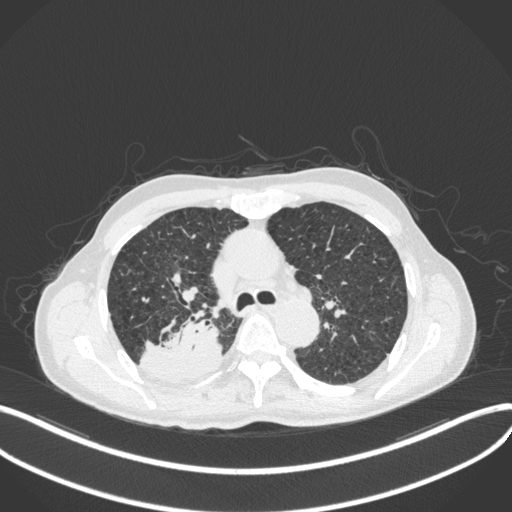
Chest CT, one axial slice; slice 305 of 423 in the series (ordered by position); lung window (W 1500 / L -600 HU); 512 × 512 image matrix. Patient: male, 79 years. Case-level facts recorded for this patient, not image findings: clinical TNM (as recorded): T3 N0 M0.
Outlined on this slice (rectangle marked by the reading radiologist):
- lung tumour (recorded histology: adenocarcinoma): bounding box [x1, y1, x2, y2] px = [139, 315, 224, 387]